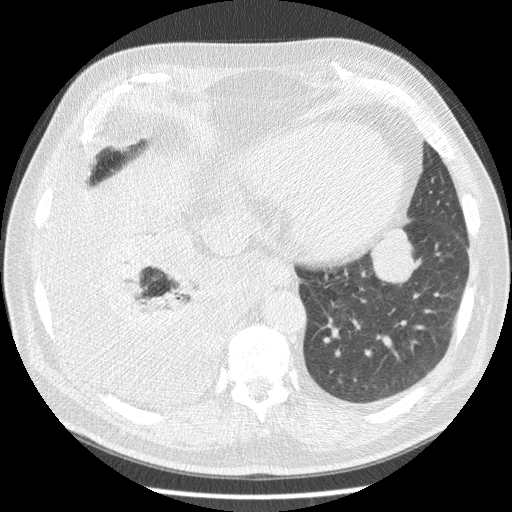
Low-dose screening chest CT, one axial slice. Slice 58 of 180 in the series (ordered by position). Reconstruction kernel STANDARD. Lung window (W 1500 / L -600 HU). 512 × 512 image matrix.
Structures marked on this image (expert manual segmentation):
- lesion 1 (tumor, lower lobe of left lung): bounding box <371,228,421,283> (left, top, right, bottom; pixels)